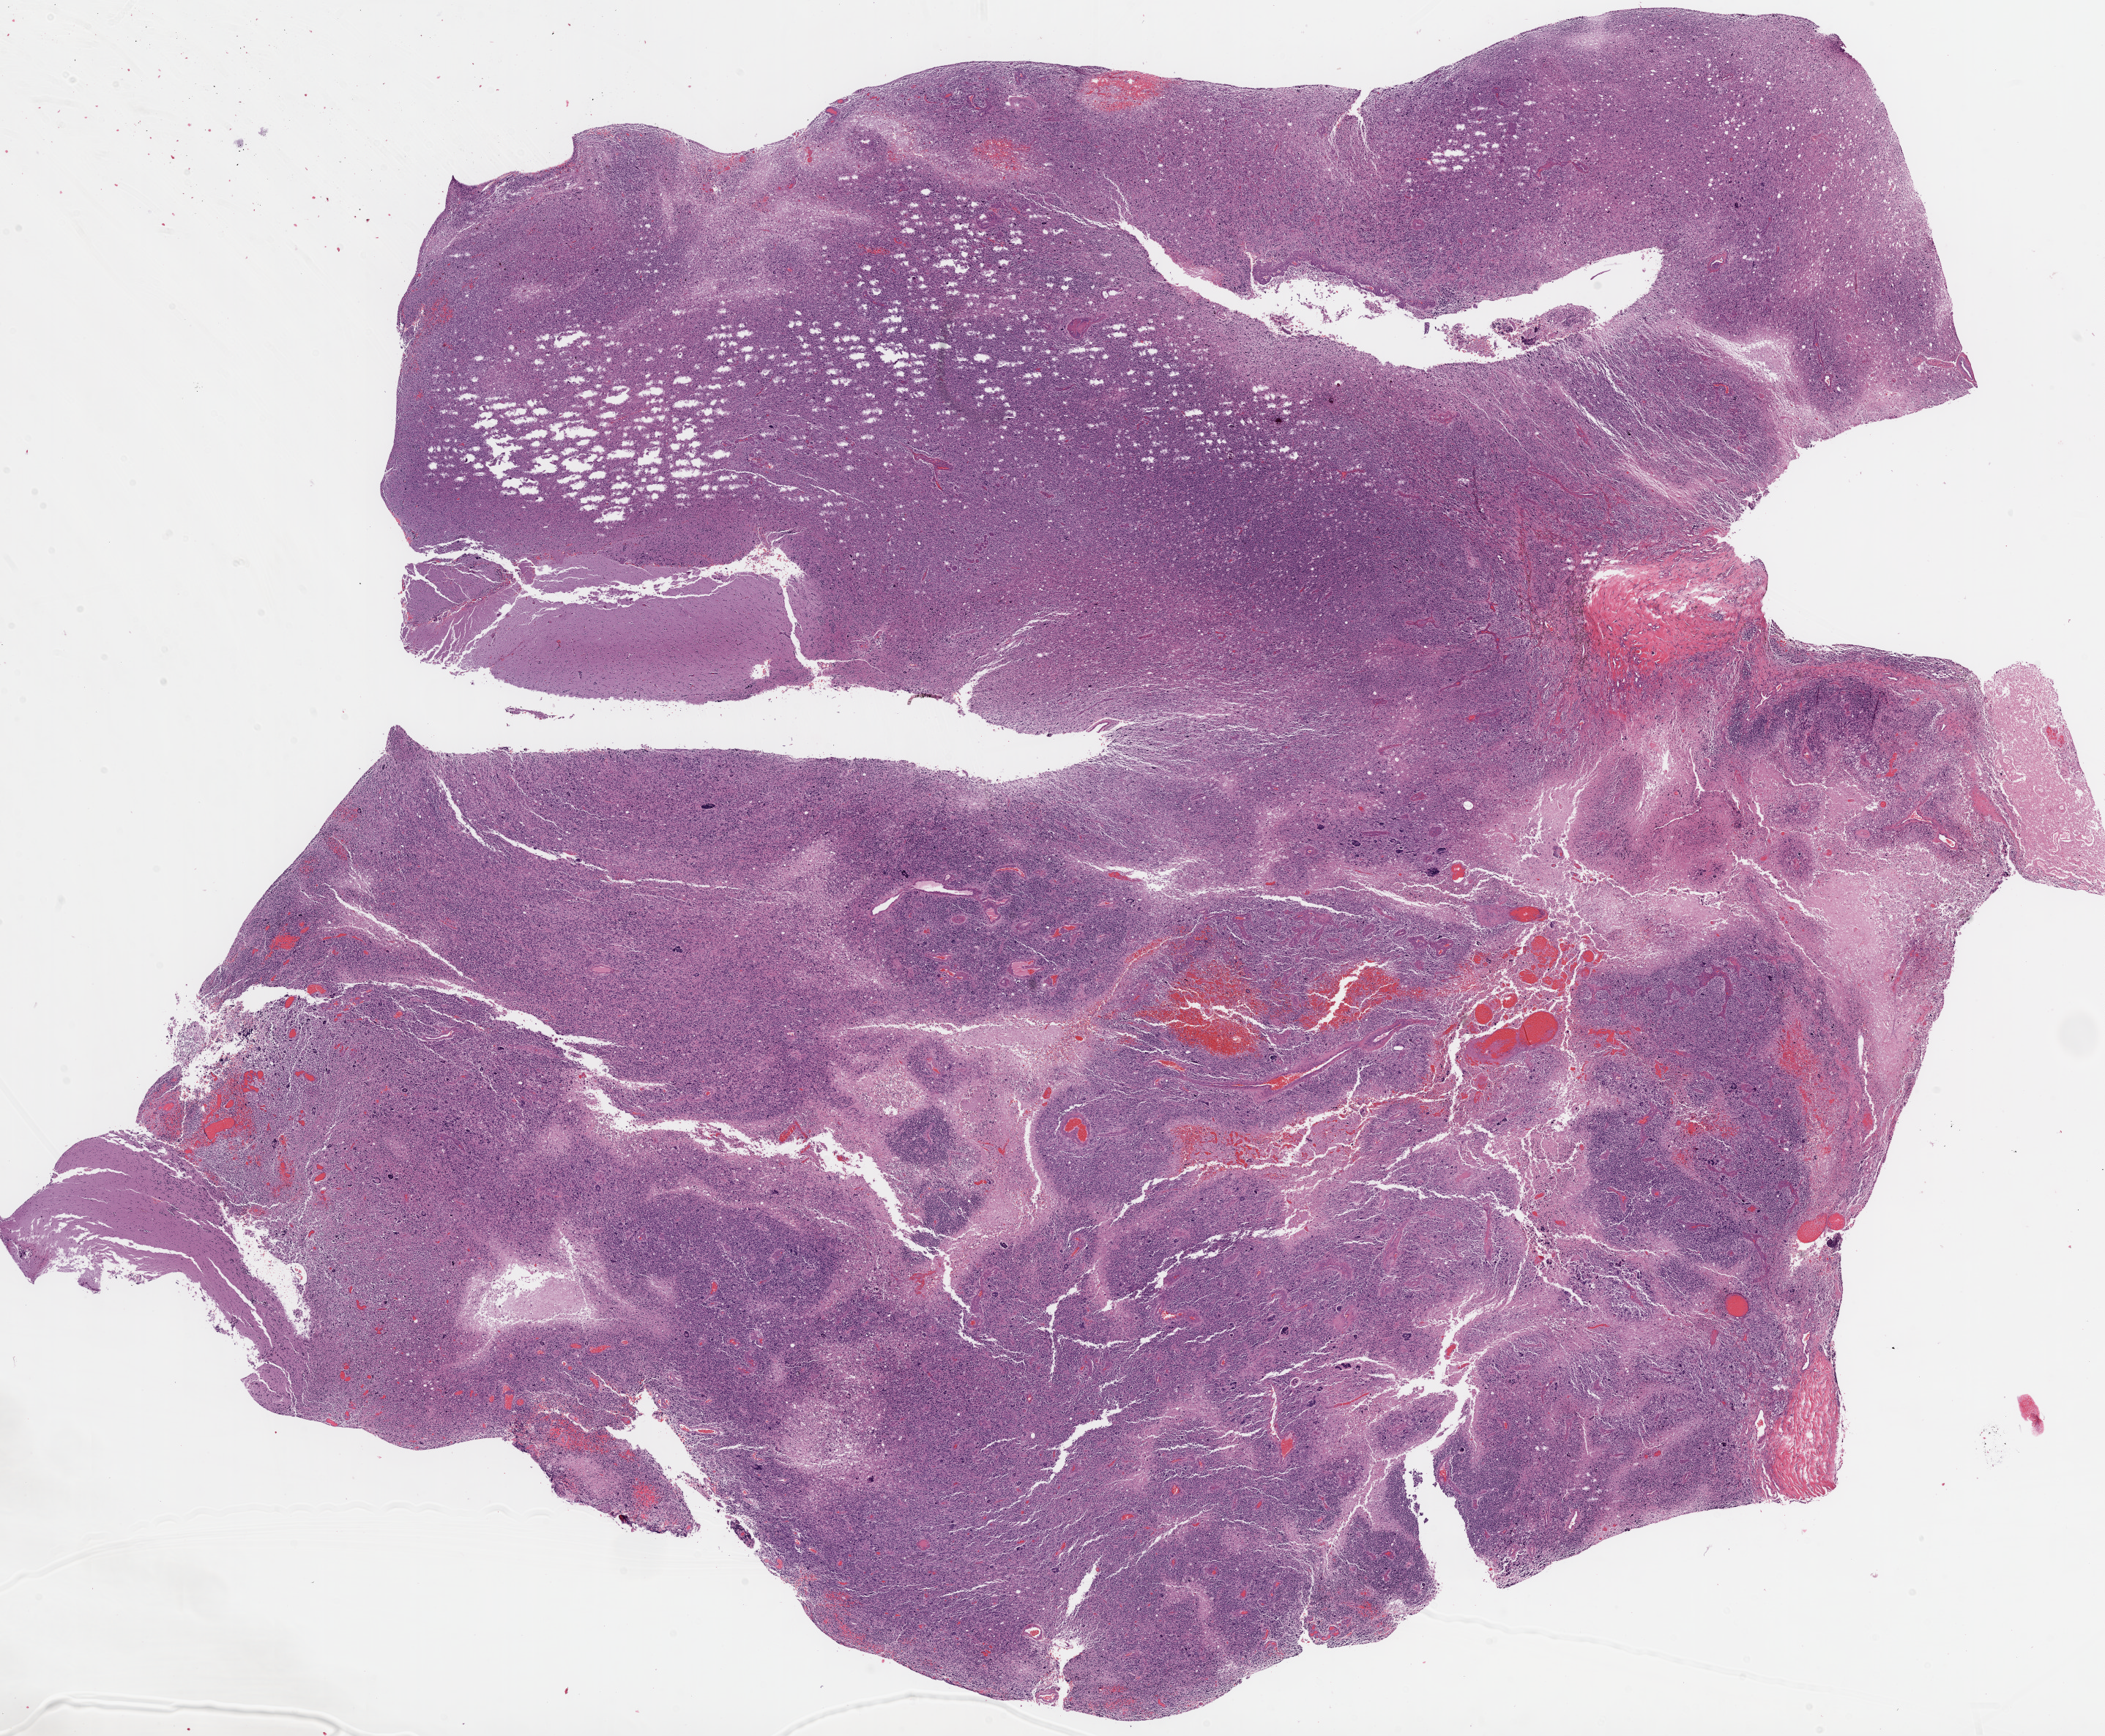
H&E-stained whole-slide image — whole scanned area (about 23.1 x 19.0 mm, from a 20x scan) shown as a low-resolution overview; FFPE section; sample: primary tumour, brain. Male, age 27 years at initial diagnosis.
Diagnosis: Glioblastoma.